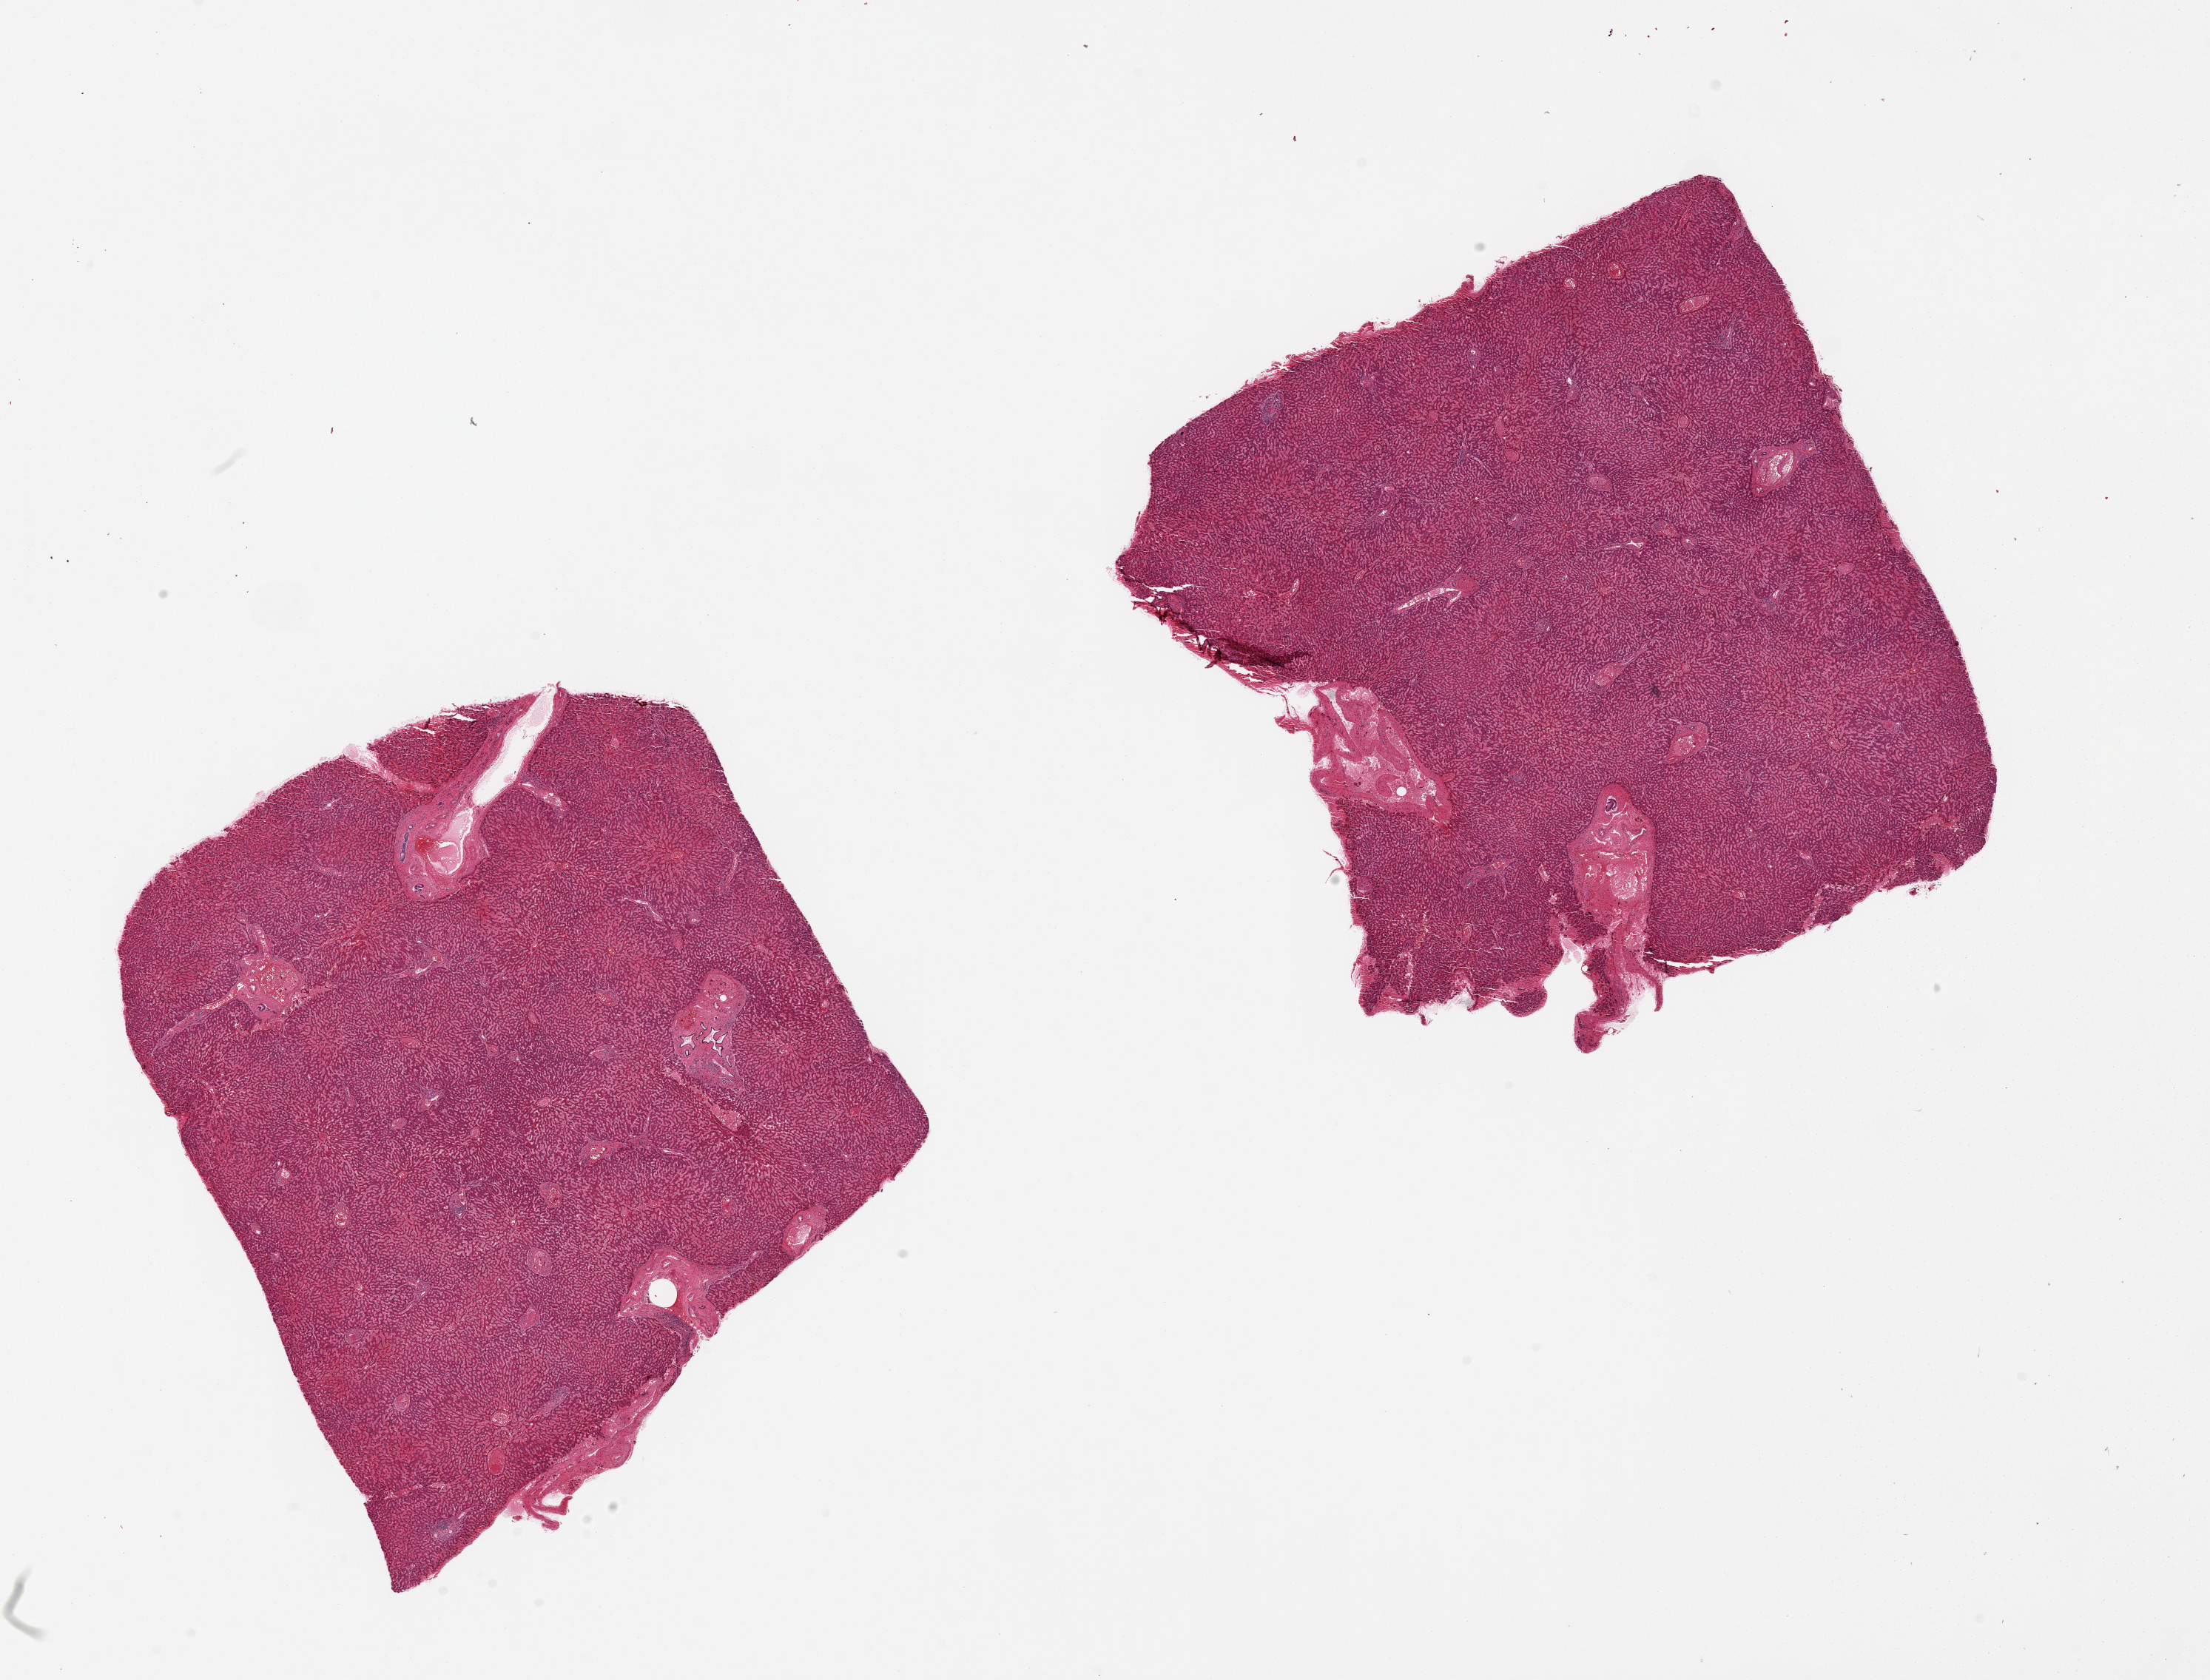
Haematoxylin and eosin whole-slide image, shown as a low-resolution overview of the whole scanned area (about 23.6 x 18.0 mm). PAXgene-fixed, paraffin-embedded tissue. Target tissue: liver. Donor tissue sample. Male donor.
Reviewer comment on this tissue sample: 2 pieces, 8x8 and 8x7mm.